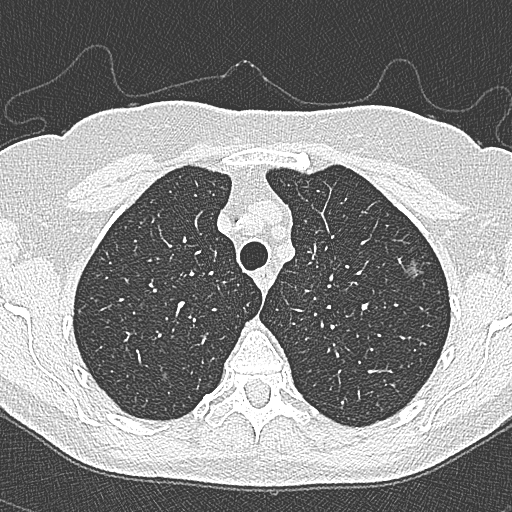
Chest CT (low-dose screening protocol), one axial image, second annual screen, lung window (W 1500 / L -600 HU), 1 mm slice thickness, lung (sharp) reconstruction kernel (B80f), slice 68 of 350 in the series. Female participant, aged 65 years at enrolment.
Expert-annotated lung lesion, box from (x=396, y=251) to (x=433, y=285) px. The screening reader recorded 4 non-calcified nodules or masses ≥4 mm on this exam; which of them this box marks is not recorded. Lung cancer was diagnosed 54 days after this screen: bronchiolo-alveolar carcinoma, non-mucinous, left upper lobe, stage IA (AJCC 6th edition), 10 mm at pathology.